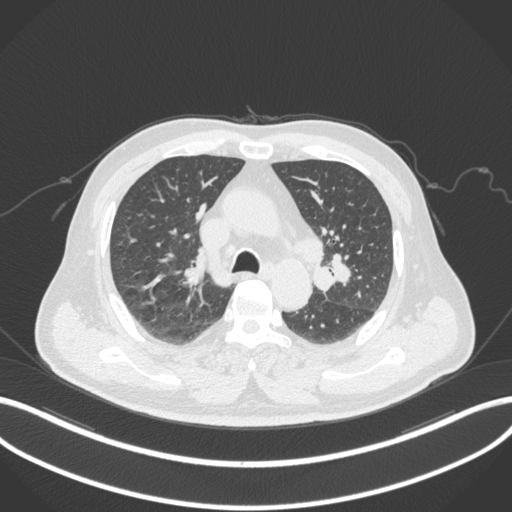
Chest CT, one axial slice; slice 201 of 286 in the series (ordered by position); reconstruction kernel B31f; 120 kVp; lung window (W 1500 / L -600 HU); 512 × 512 image matrix, field of view 400 × 400 mm. Patient: male, 67 years. Case-level facts recorded for this patient, not image findings: clinical TNM (as recorded): T2a N1 M0; histopathological grade: G3.
Annotated regions visible in this slice (bounding box drawn by a radiologist):
- lung tumour (recorded histology: adenocarcinoma): bounding box (x1, y1, x2, y2) in pixels: (310, 255, 351, 296)